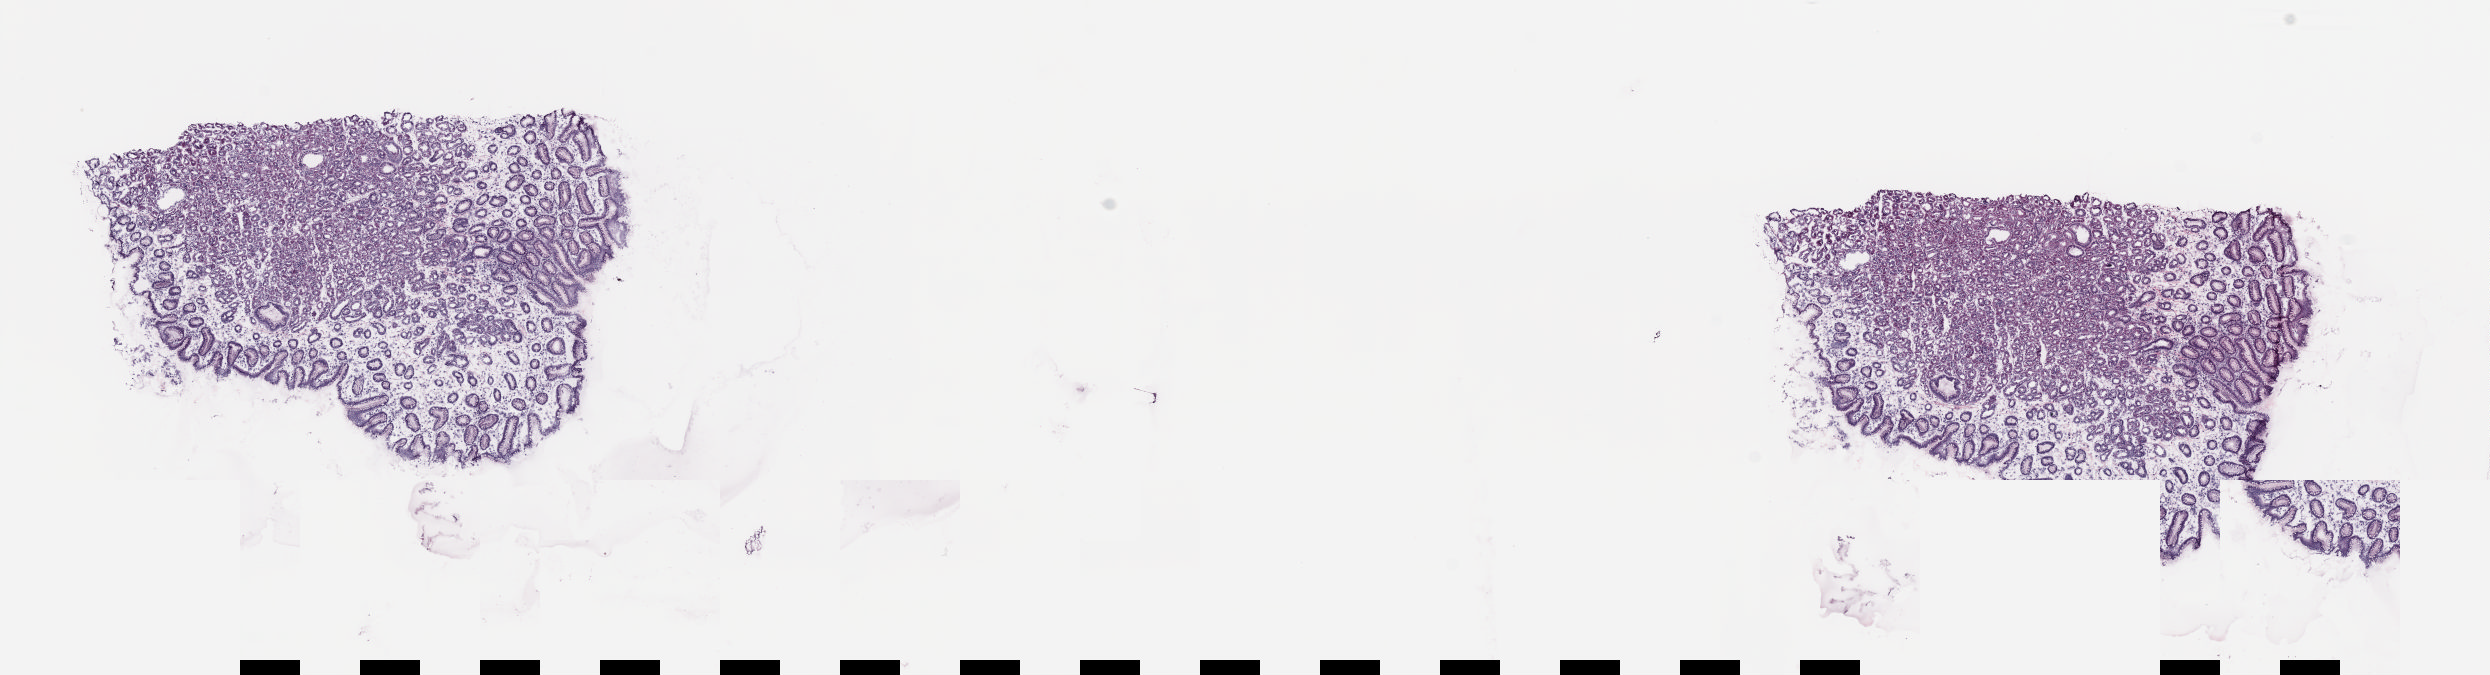
Whole-slide histology image, Hematoxylin and eosin (H&E) stained, a low-resolution overview of the entire scanned area, about 19.7 x 5.3 mm, frozen section from the top of the tissue portion, solid tissue normal (non-tumour tissue) sample from the esophagus. Male patient; age at initial diagnosis 74 years. Pathologist review of this section (percent, as recorded): tumour cells 0%, tumour nuclei 0%, normal cells 70%, stromal cells 30%, necrosis 0%. Infiltration values recorded for this section: lymphocyte infiltration 3%, monocyte infiltration 0%, neutrophil infiltration 0%.
This section: solid tissue normal sample (biorepository sample class). Patient diagnosis: Adenocarcinoma, NOS (lower third of esophagus).